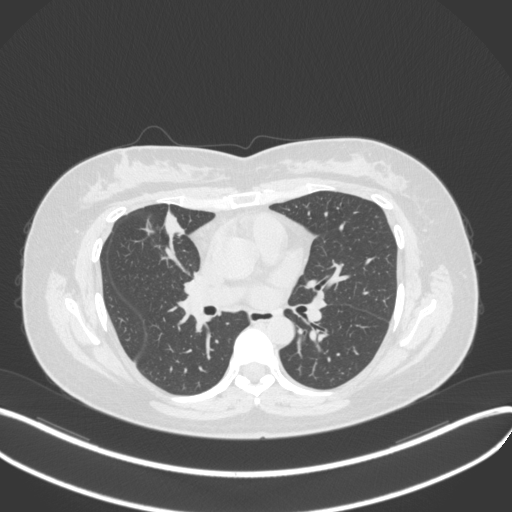
Chest CT, one axial slice. Position 169 of 272 along the scan axis. Reconstruction kernel B31f. Lung window (W 1500 / L -600 HU). 1 mm slice thickness. 512 × 512 image matrix, field of view 400 × 400 mm. Patient: female, 42 years. From the clinical record (not read from this slice): clinical TNM (as recorded): T1b N0 M0.
Annotated regions visible in this slice (rectangle marked by the reading radiologist):
- lung tumour (recorded histology: adenocarcinoma): bounding box [x1, y1, x2, y2] px = [157, 205, 188, 247]